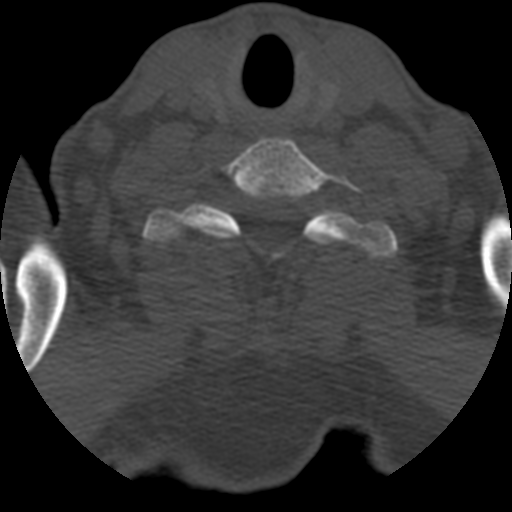
CT including the spine, one axial slice. Position 526 of 708 along the scan axis. Reconstruction kernel STANDARD. 120 kVp. One of 3 acquisitions stored at this slice position. Bone window (W 1800 / L 400 HU). 1.25 mm slice thickness. 512 × 512 image matrix, field of view 160 × 160 mm. Patient age 55 years. Case-level facts recorded for this patient, not image findings: primary cancer: colon.
Outlined on this slice (semi-automatically segmented with operator editing):
- T1 vertebra: bounding box [x1, y1, x2, y2] px = [142, 202, 397, 260]